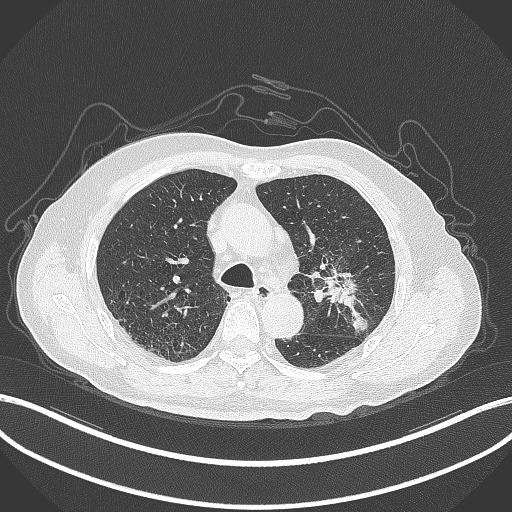
Chest CT, one axial slice. Slice 193 of 331 in the series (ordered by position). 120 kVp. Lung window (W 1500 / L -600 HU). 1 mm slice thickness. 512 × 512 image matrix, field of view 400 × 400 mm. Male patient, age 79 years. From the clinical record (not read from this slice): clinical TNM (as recorded): T2a N1 M1; histopathological grade: G3.
Outlined on this slice (bounding box drawn by a radiologist):
- lung tumour (recorded histology: adenocarcinoma): bounding box (x1, y1, x2, y2) in pixels: (321, 265, 373, 334)